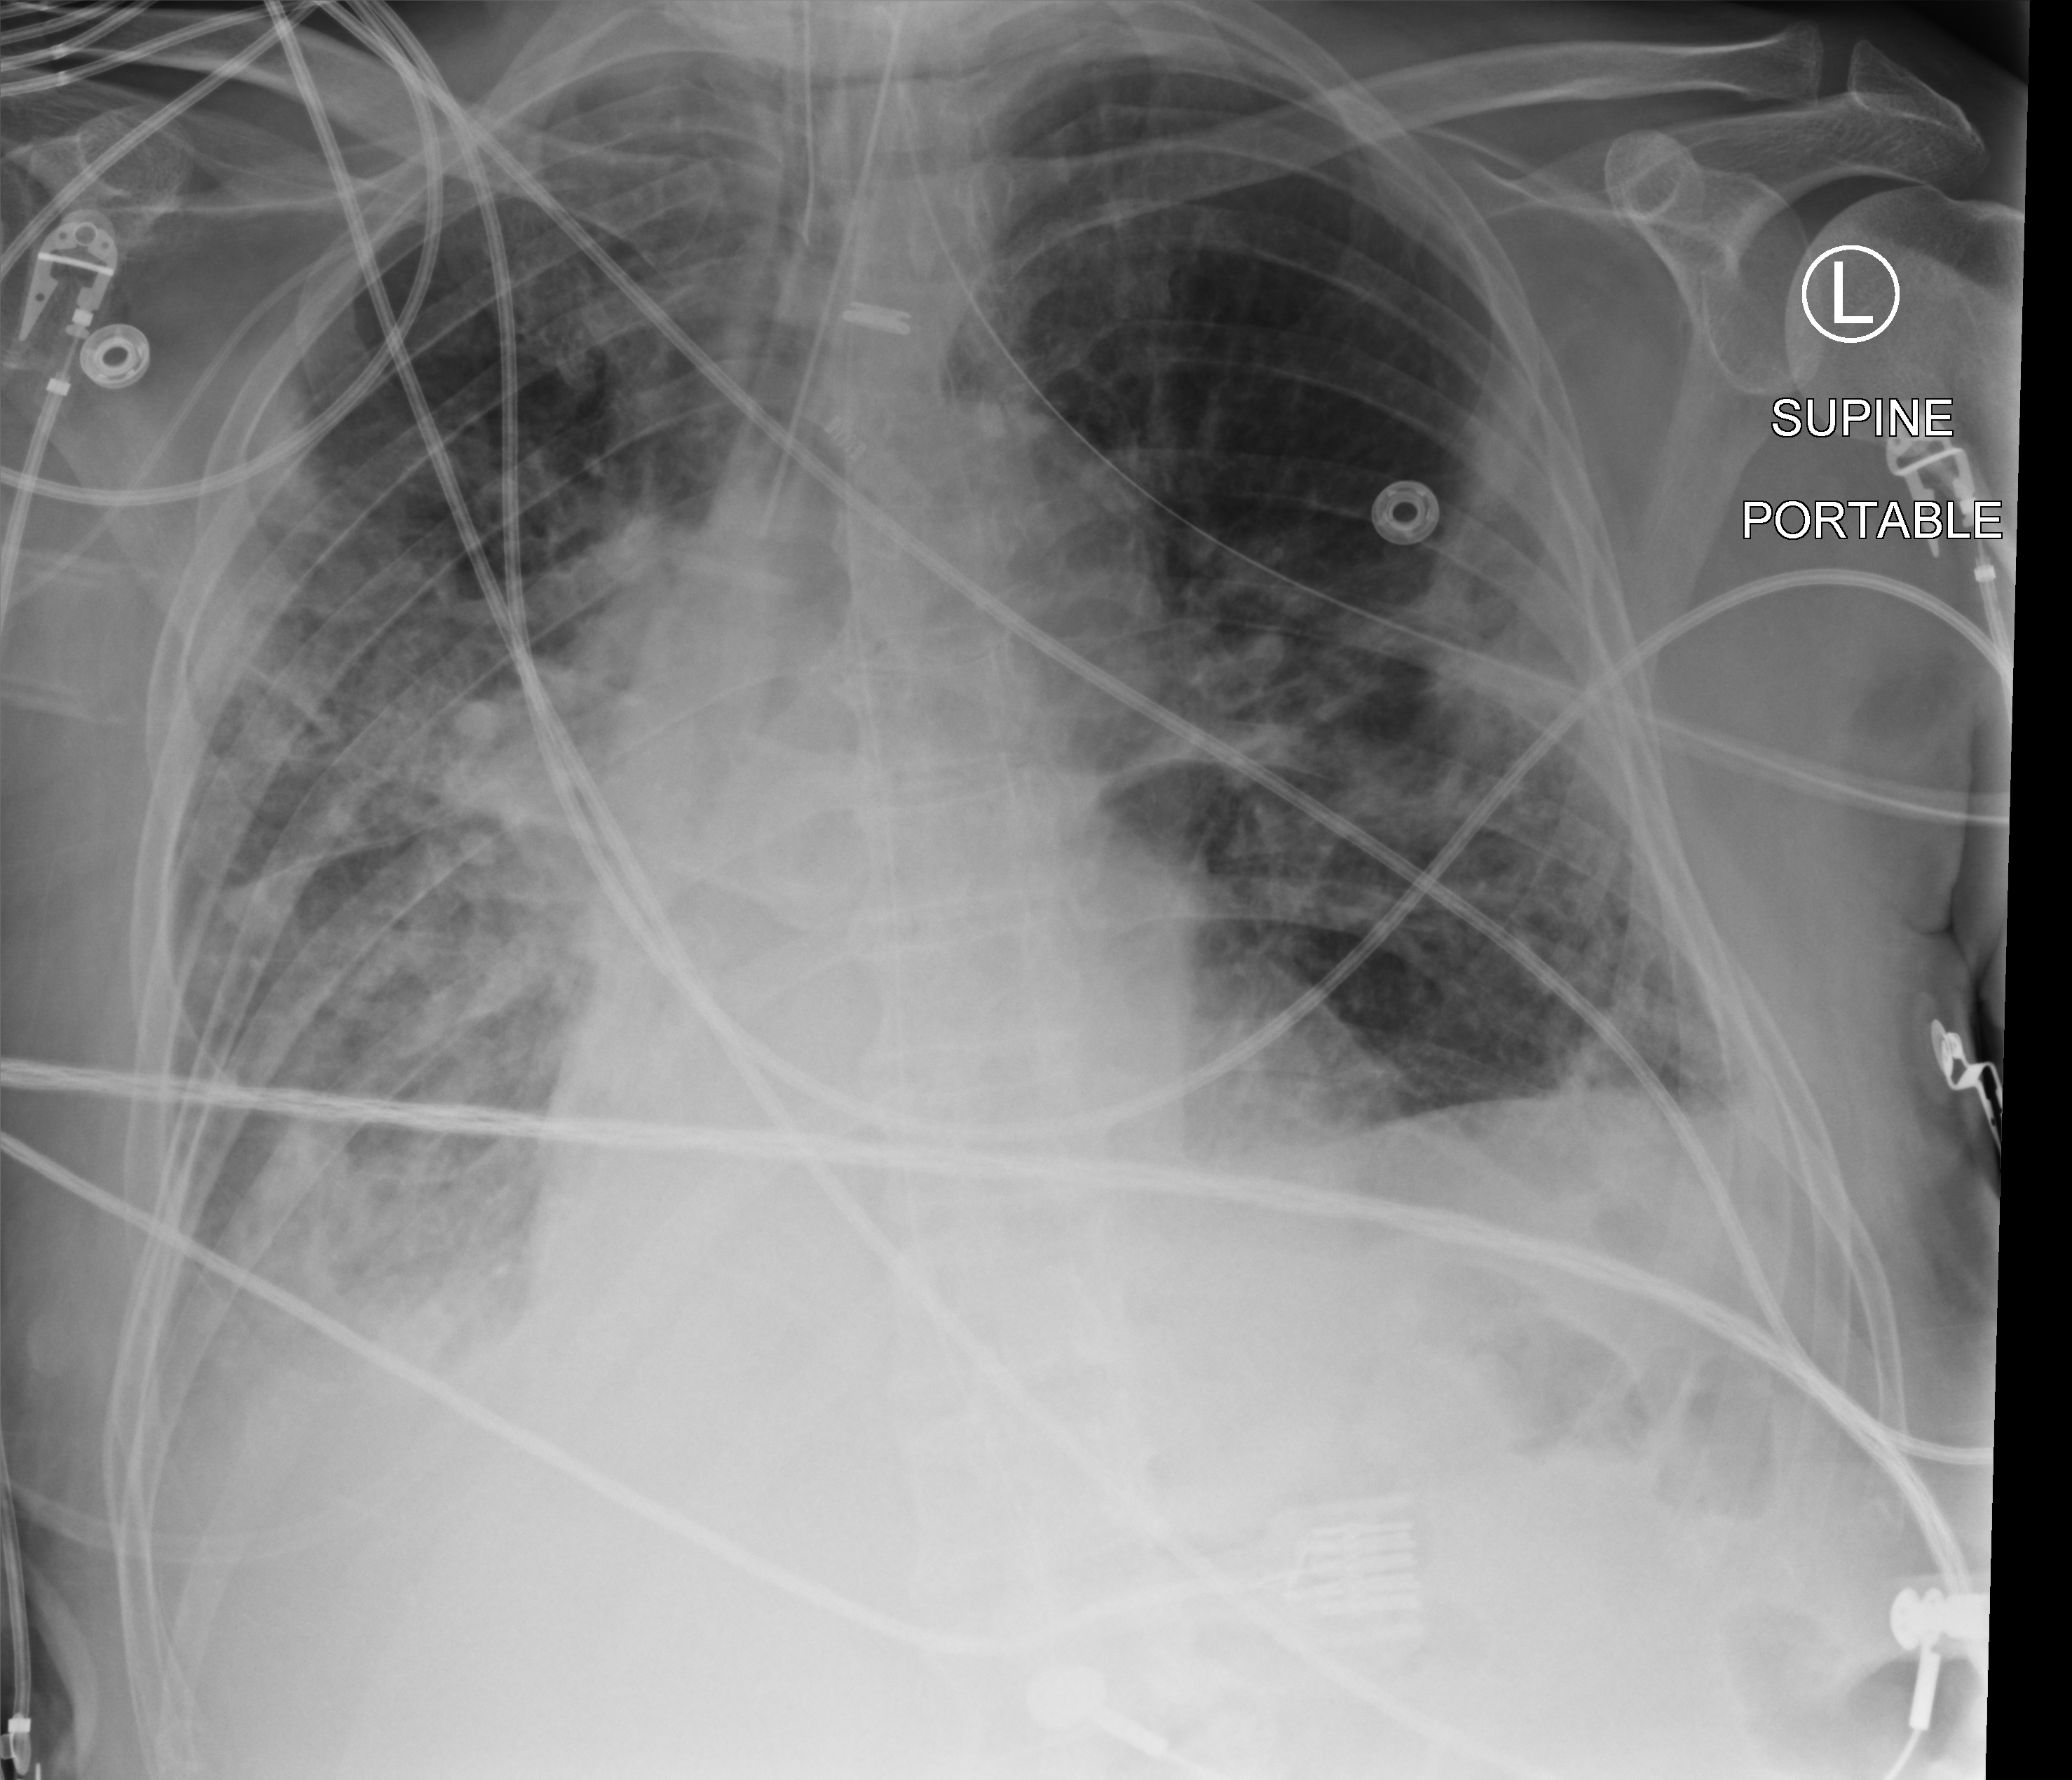
Portable chest radiograph; anteroposterior (AP) projection. Patient hospitalised with COVID-19; male, aged 75–90 years.
From the hospital-stay record, not from the radiograph (when in the stay this image was taken is not recorded): mechanically ventilated during this hospital stay: yes; admitted to intensive care during this hospital stay: yes.